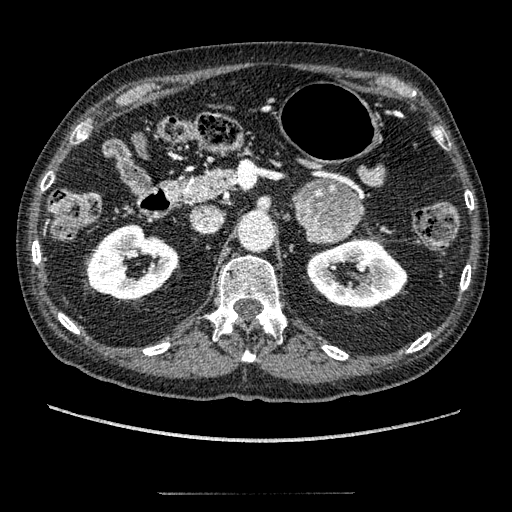
Contrast-enhanced abdominal CT, one axial slice; position 117 of 274 along the scan axis; 120 kVp; soft-tissue window (W 400 / L 40 HU); 512 × 512 image matrix. Male patient, age 69 years. Case-level facts recorded for this patient, not image findings: diagnosis: adrenocortical carcinoma; tumour side: left adrenal; tumour size at pathology: 6.1 cm; Ki-67 index: 10 %.
Outlined on this slice (semi-automatically segmented with operator editing):
- mass: bounding box <295,179,363,243> (left, top, right, bottom; pixels)